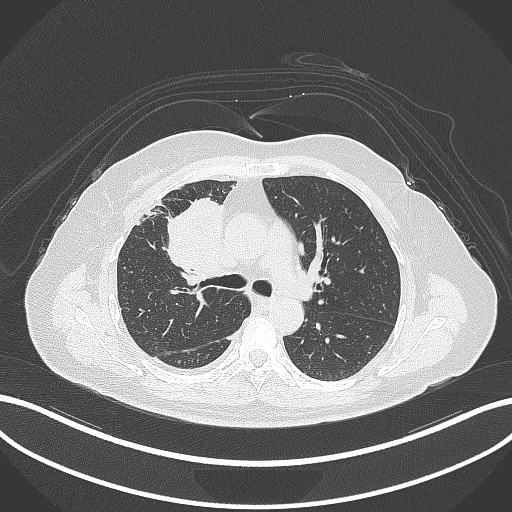
Chest CT, one axial slice. Position 179 of 305 along the scan axis. Lung window (W 1500 / L -600 HU). 1 mm slice thickness. 512 × 512 image matrix, field of view 400 × 400 mm. Female patient, age 52 years. Case-level facts recorded for this patient, not image findings: clinical TNM (as recorded): T3 N1 M1.
Annotated regions visible in this slice (bounding box drawn by a radiologist):
- lung tumour (recorded histology: adenocarcinoma): bounding box [x1, y1, x2, y2] px = [157, 193, 229, 284]